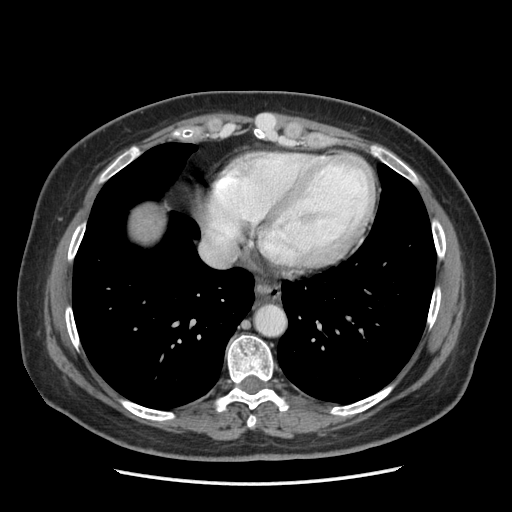
Contrast-enhanced abdominal CT (liver protocol), one axial slice. Slice 177 of 185 in the series (ordered by position). Soft-tissue window (W 400 / L 40 HU). 2.5 mm slice thickness. 512 × 512 image matrix. Case-level facts recorded for this patient, not image findings: diagnosis: hepatocellular carcinoma (patient treated with transarterial chemoembolisation; whether this scan precedes or follows treatment is not stated here); TNM stage (as recorded): Stage-I; Child-Pugh class: A.
Annotated regions visible in this slice (semi-automatic segmentation, software-assisted and operator-edited):
- liver parenchyma outside the tumour (the mass and vessels are separate outlines, so this box may not span the whole liver): bounding box [x1, y1, x2, y2] px = [132, 208, 162, 240]